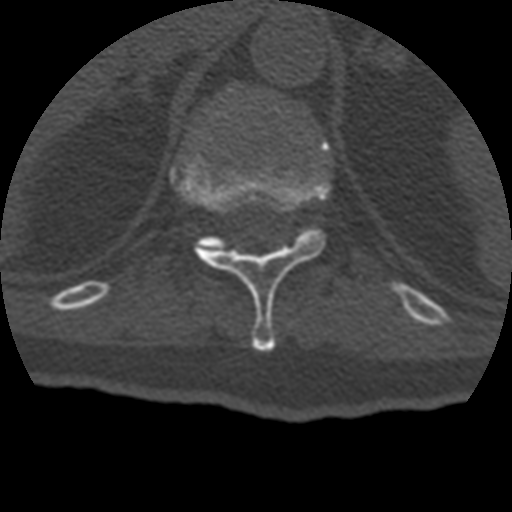
CT including the spine, one axial slice. Reconstruction kernel STANDARD. 120 kVp. Bone window (W 1800 / L 400 HU). 1.25 mm slice thickness. 512 × 512 image matrix, field of view 160 × 160 mm. Patient age 69 years. Case-level facts recorded for this patient, not image findings: primary cancer: prostate.
Outlined on this slice (semi-automatically segmented with operator editing):
- T11 vertebra: bounding box <176,155,329,351> (left, top, right, bottom; pixels)
- T12 vertebra: <204,87,294,249>